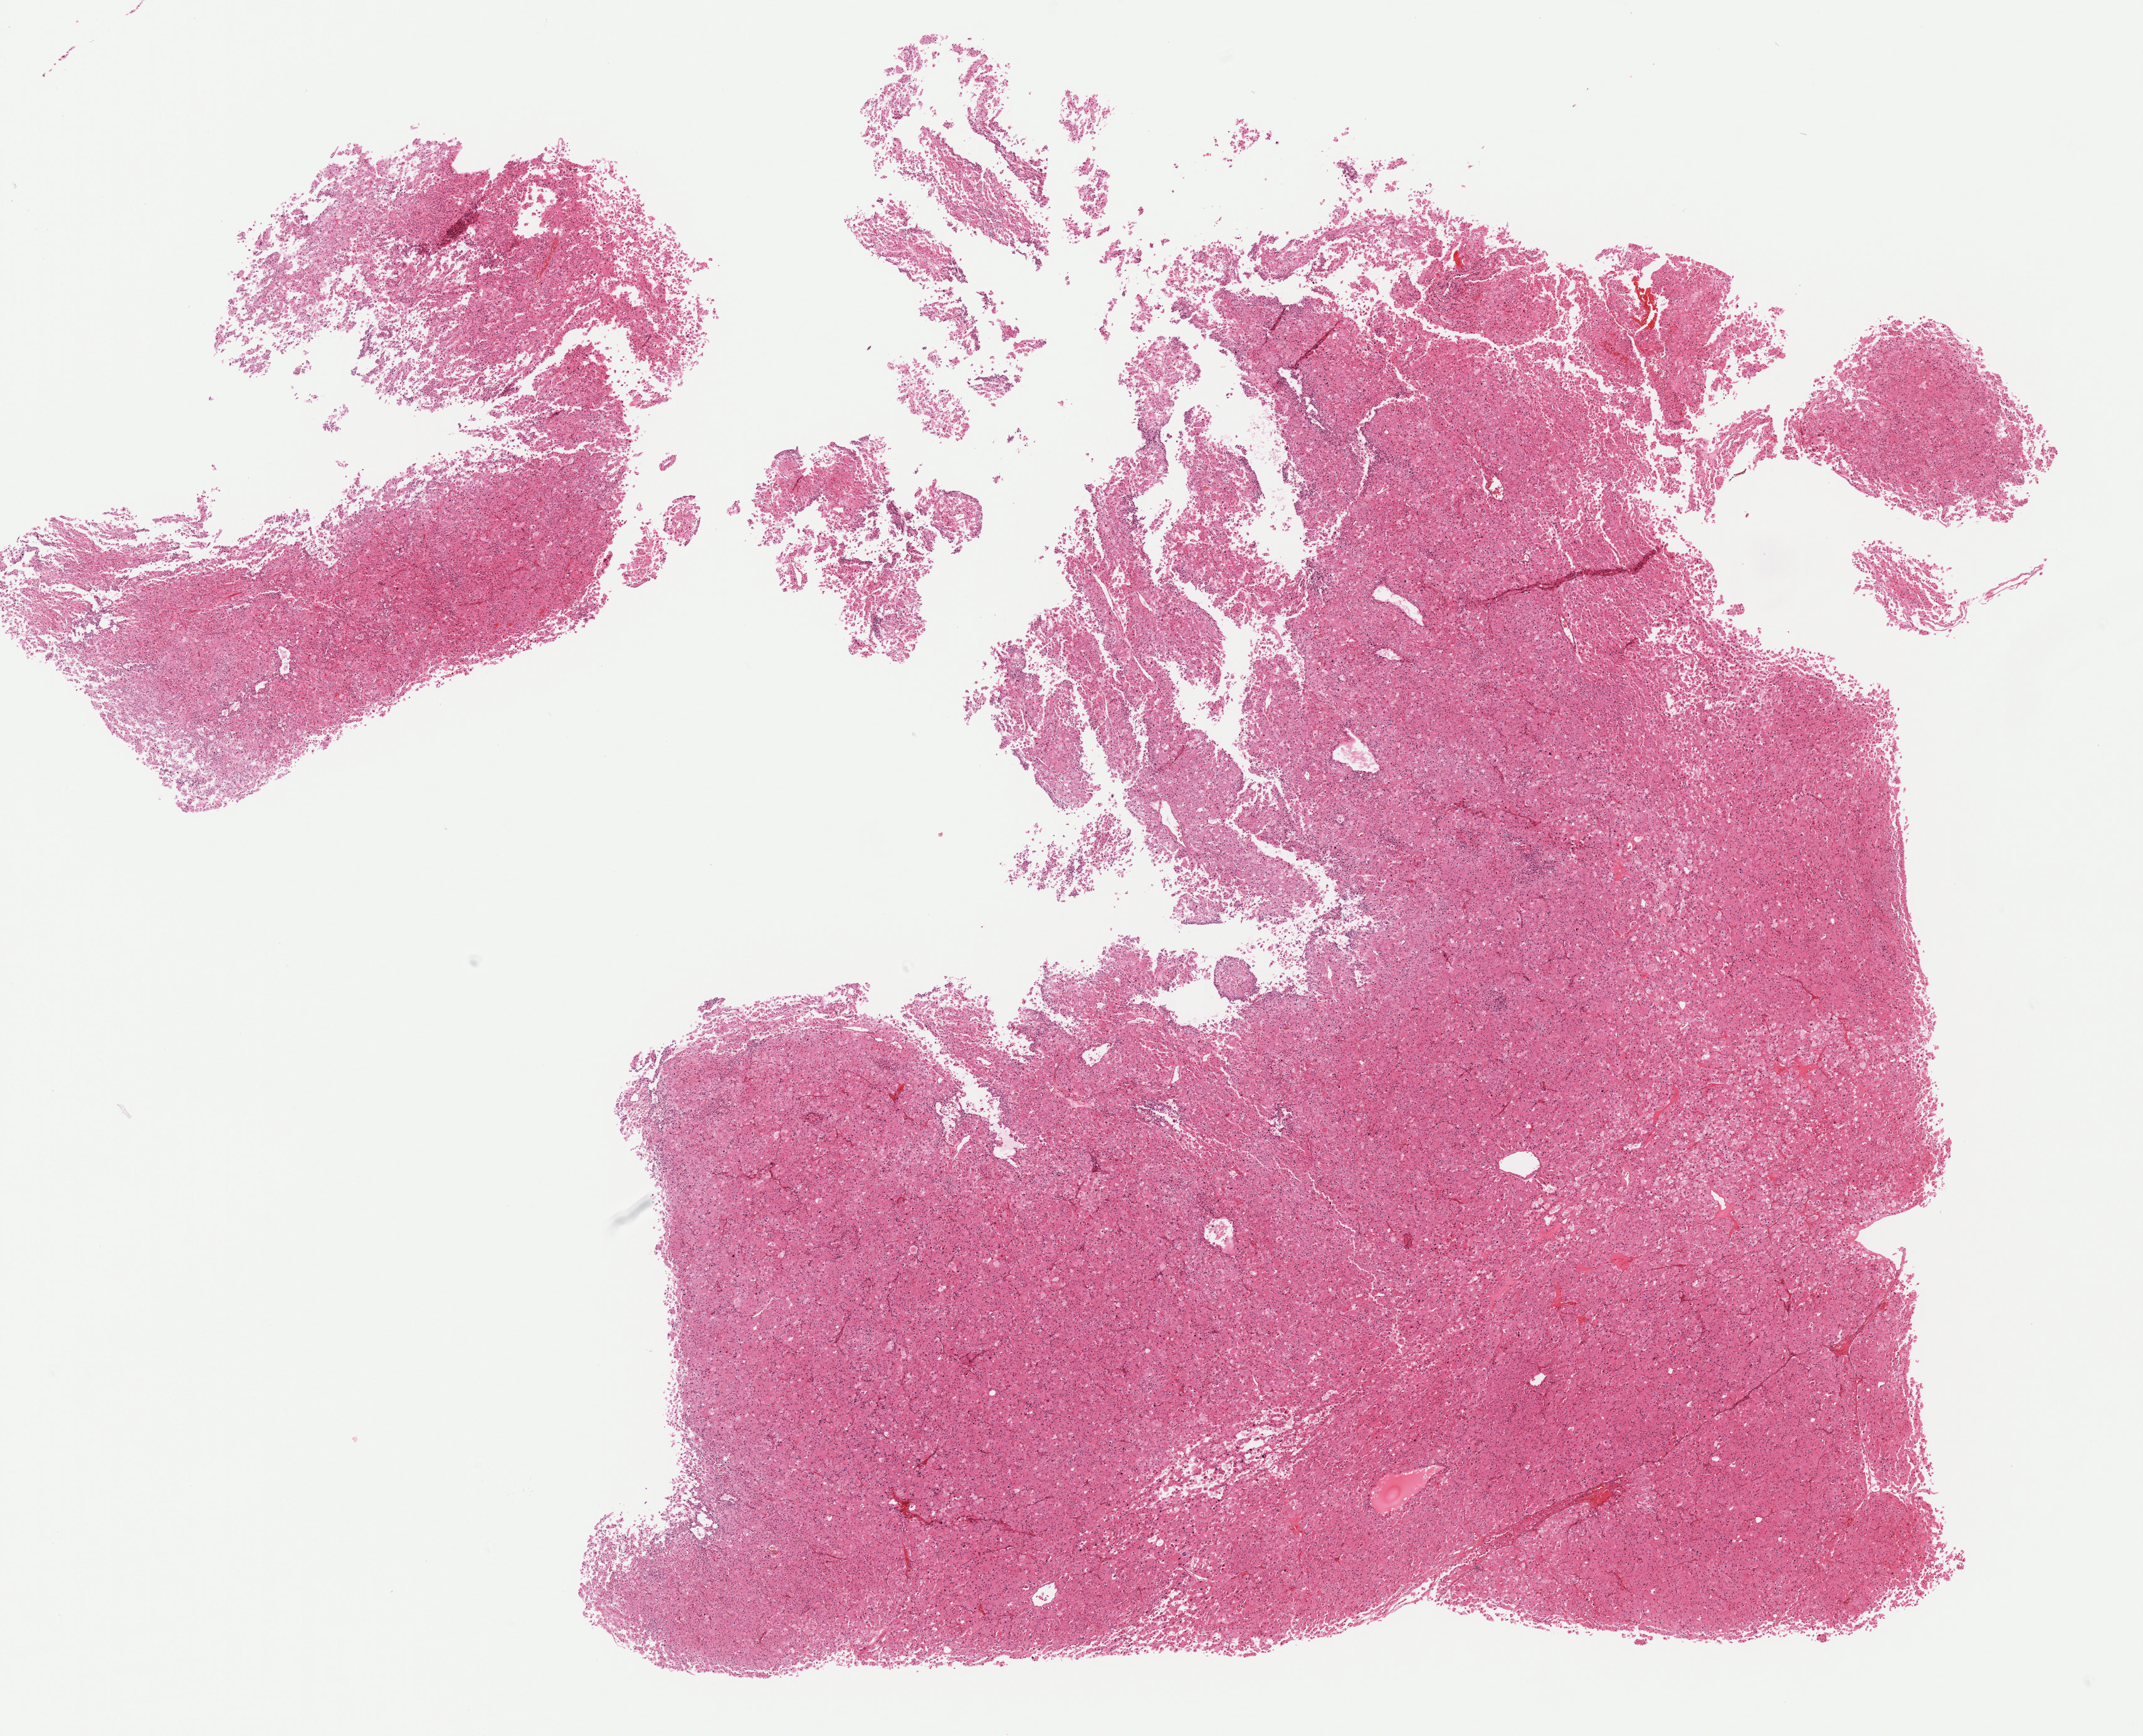
Digitized Hematoxylin and eosin (H&E) stained tissue section (whole slide) — shown as a low-resolution overview of the whole scanned area (about 13.8 x 11.2 mm, slide scanned at 40x). Formalin-fixed paraffin-embedded (FFPE) diagnostic section. Kidney, primary tumour sample. Patient: female, age at initial diagnosis 47 years.
Histologic diagnosis: Renal cell carcinoma, chromophobe type.